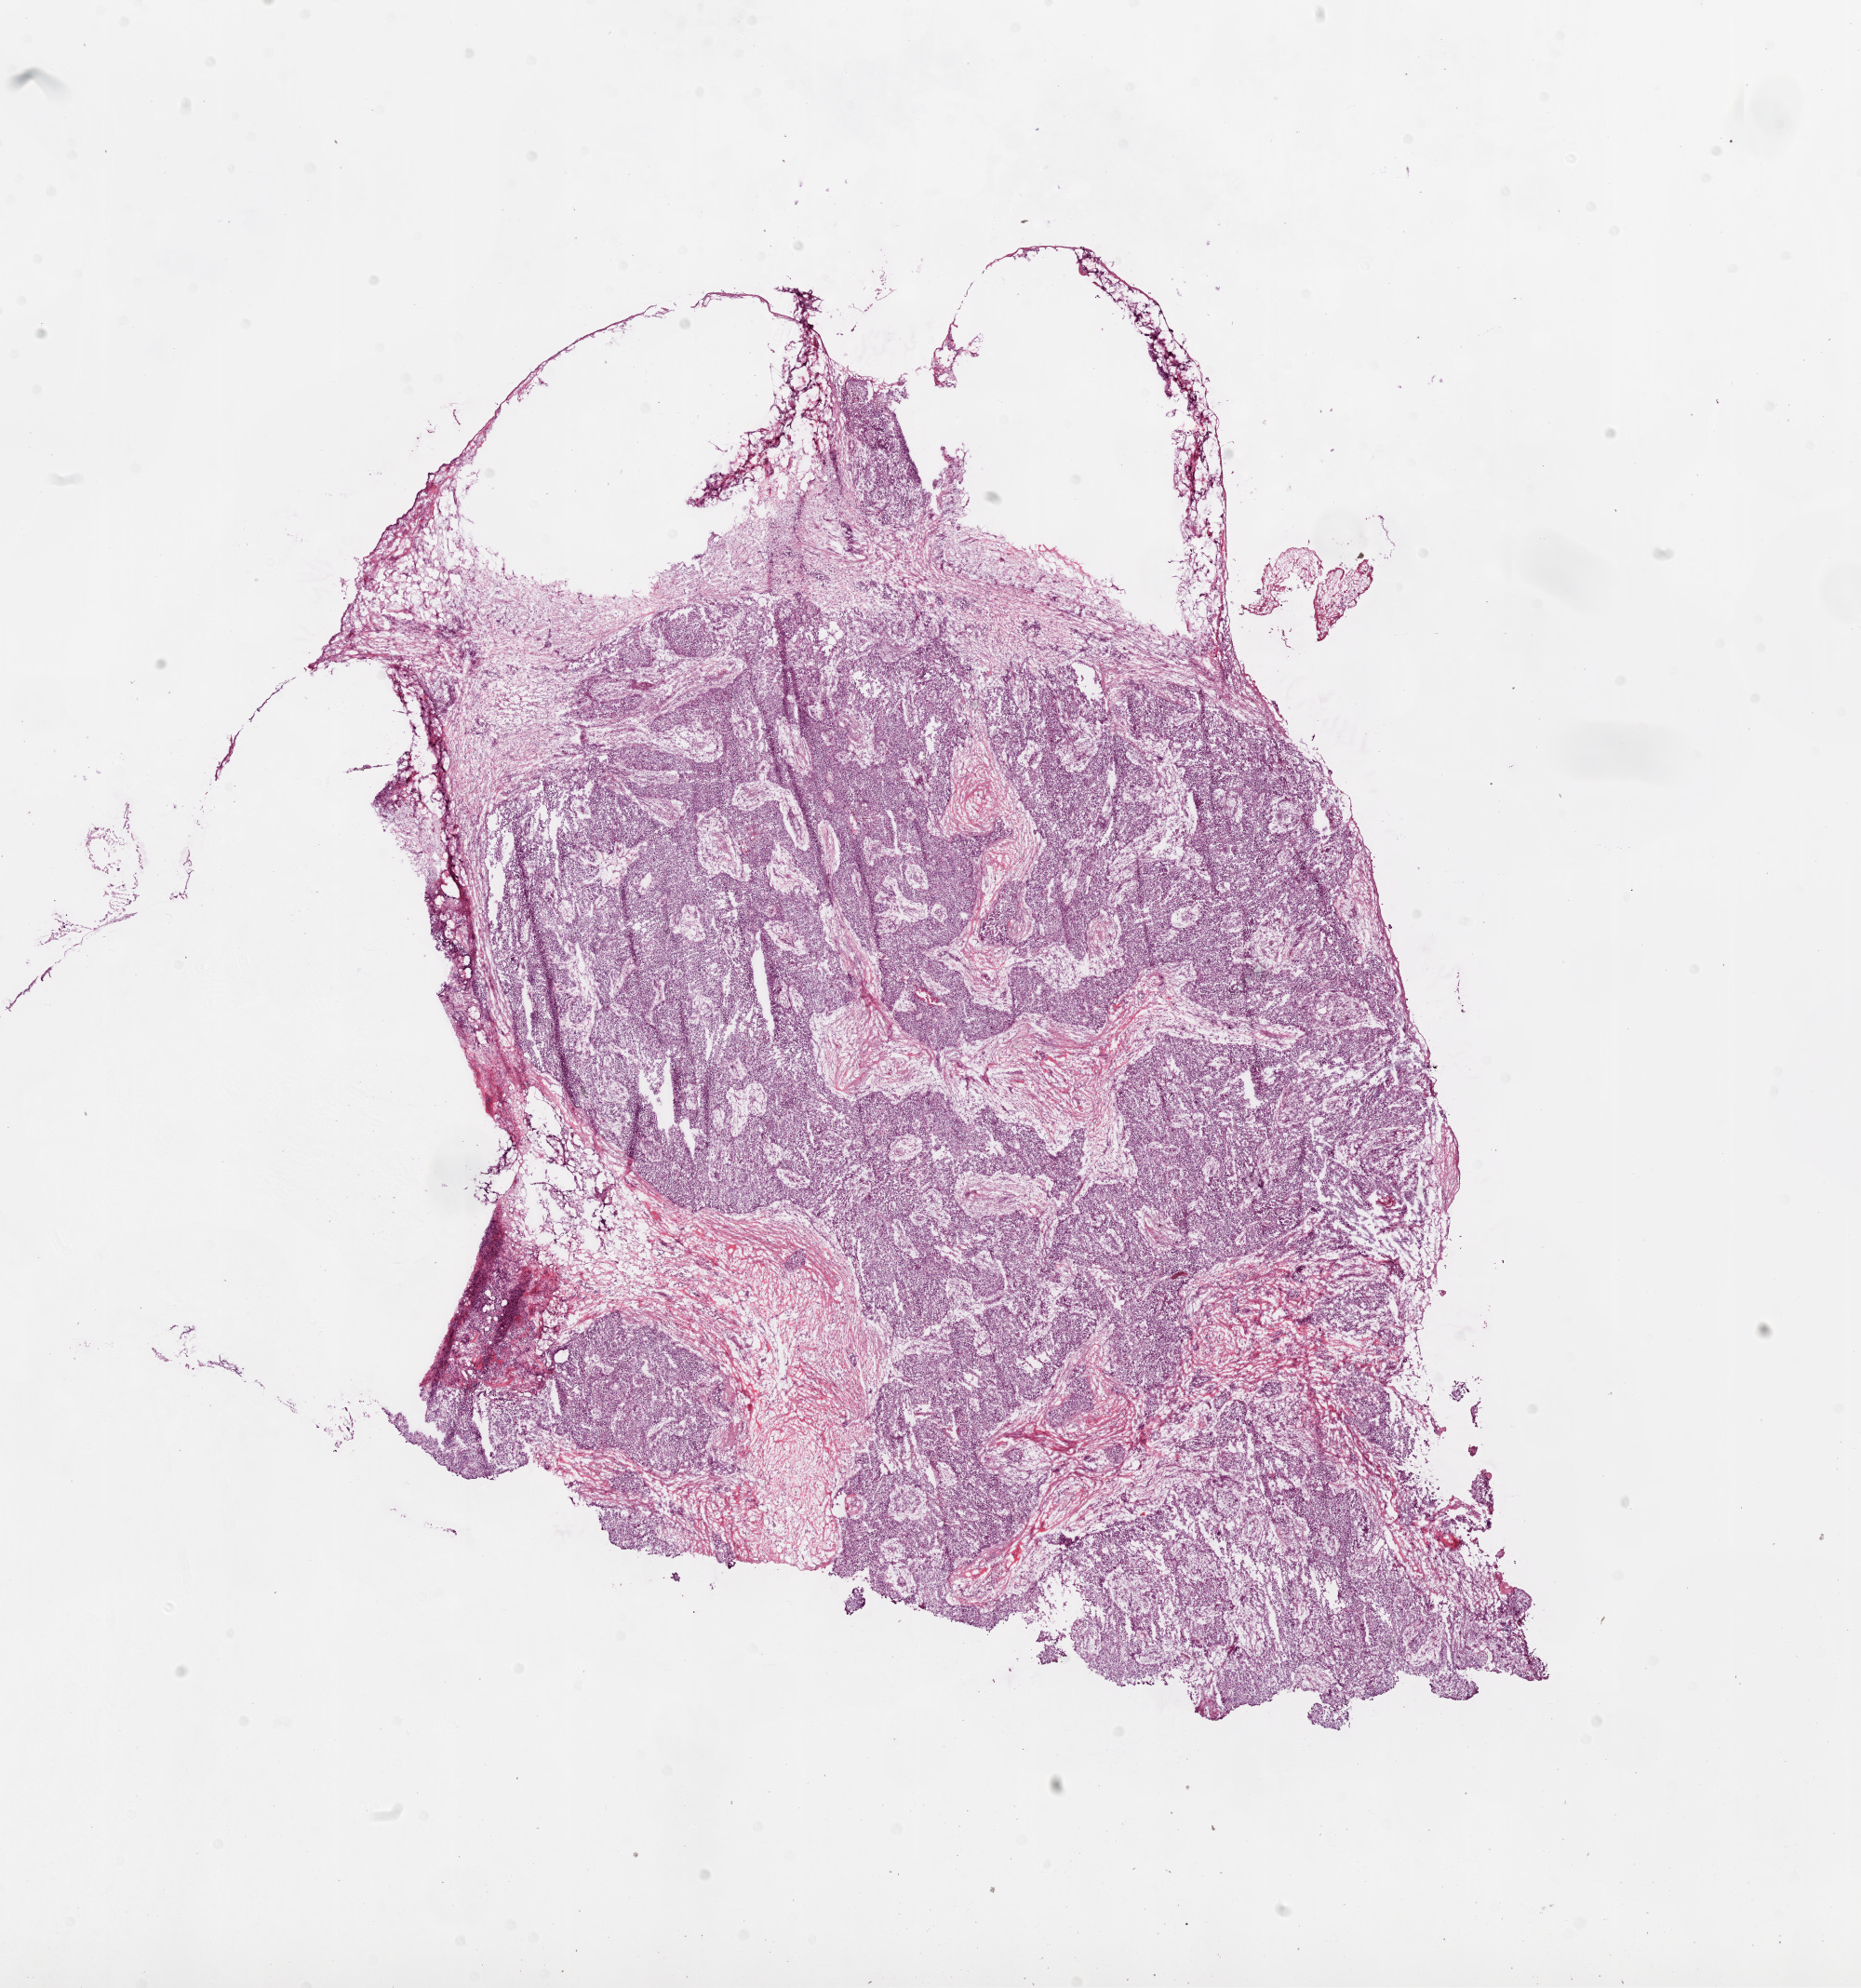
Hematoxylin and eosin (H&E) stained whole-slide image — shown as a low-resolution overview of the whole scanned area (about 16.0 x 17.1 mm, from a 20x scan). Frozen section. Ovary, primary tumour sample. Female patient; age at initial diagnosis 54 years. Histologic grade: G2 (moderately differentiated). Pathologist review of this section (percent, as recorded): tumour cells 60%, tumour nuclei 90%, normal cells 0%, stromal cells 35%, necrosis 5%.
* diagnosis: Serous cystadenocarcinoma, NOS
* FIGO stage: IIIC
* laterality: bilateral